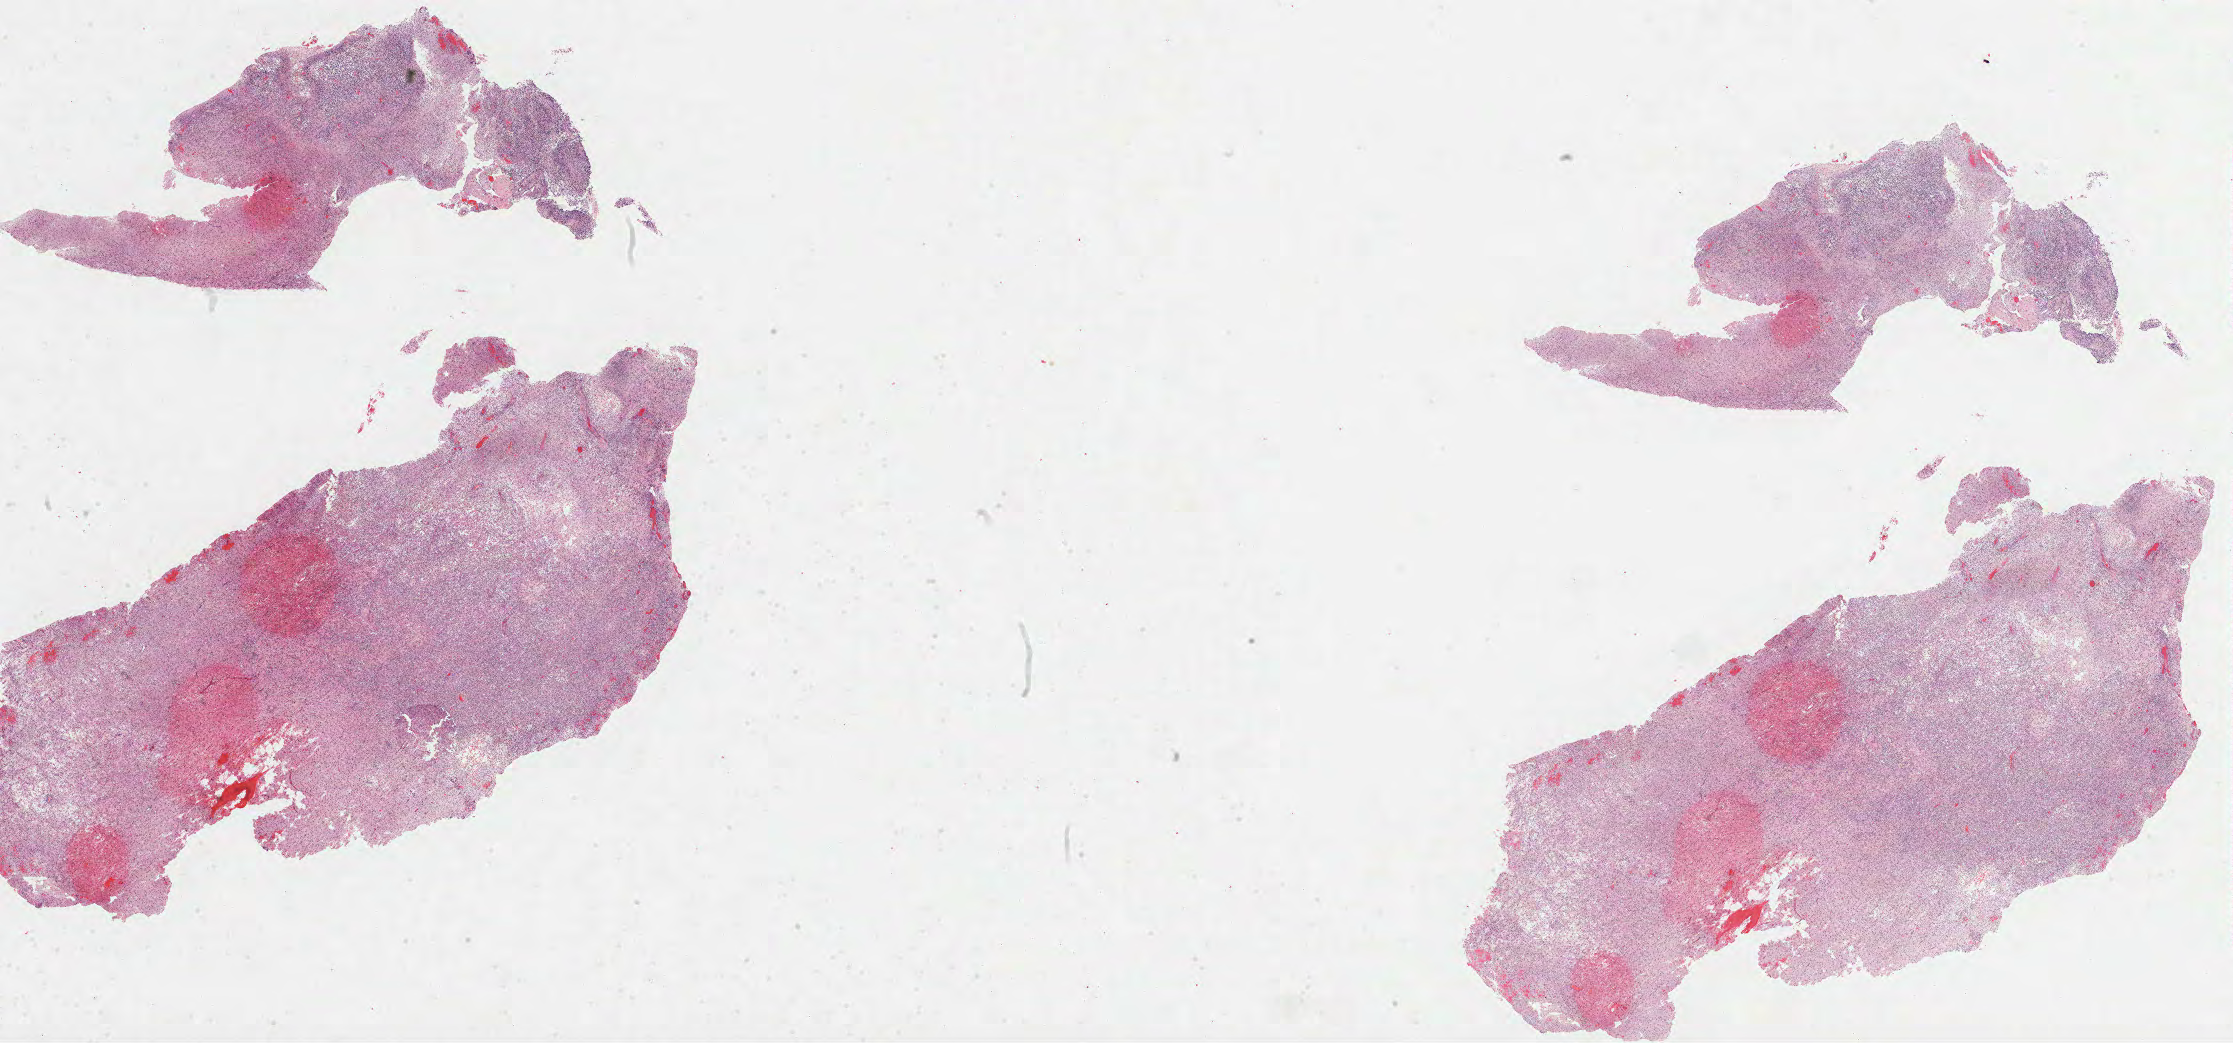
Whole-slide histology image, Hematoxylin and eosin (H&E) stained — whole scanned area (about 36.0 x 16.8 mm) shown as a low-resolution overview. FFPE section. Brain, primary tumour sample. Patient: male, age at initial diagnosis 83 years.
• diagnosis: Glioblastoma